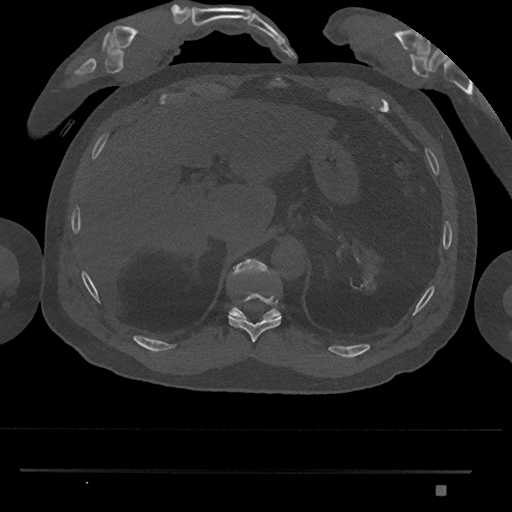
CT including the spine, one axial slice. Position 984 of 1134 along the scan axis. Reconstruction kernel Br40s/3. Bone window (W 1800 / L 400 HU). 0.5 mm slice thickness. 512 × 512 image matrix, field of view 429 × 429 mm. Patient: male, 65 years. Case-level facts recorded for this patient, not image findings: primary cancer: prostate.
Annotated regions visible in this slice (semi-automatically segmented with operator editing):
- T10 vertebra: bounding box [x1, y1, x2, y2] px = [228, 294, 282, 343]
- T11 vertebra: [228, 259, 281, 320]